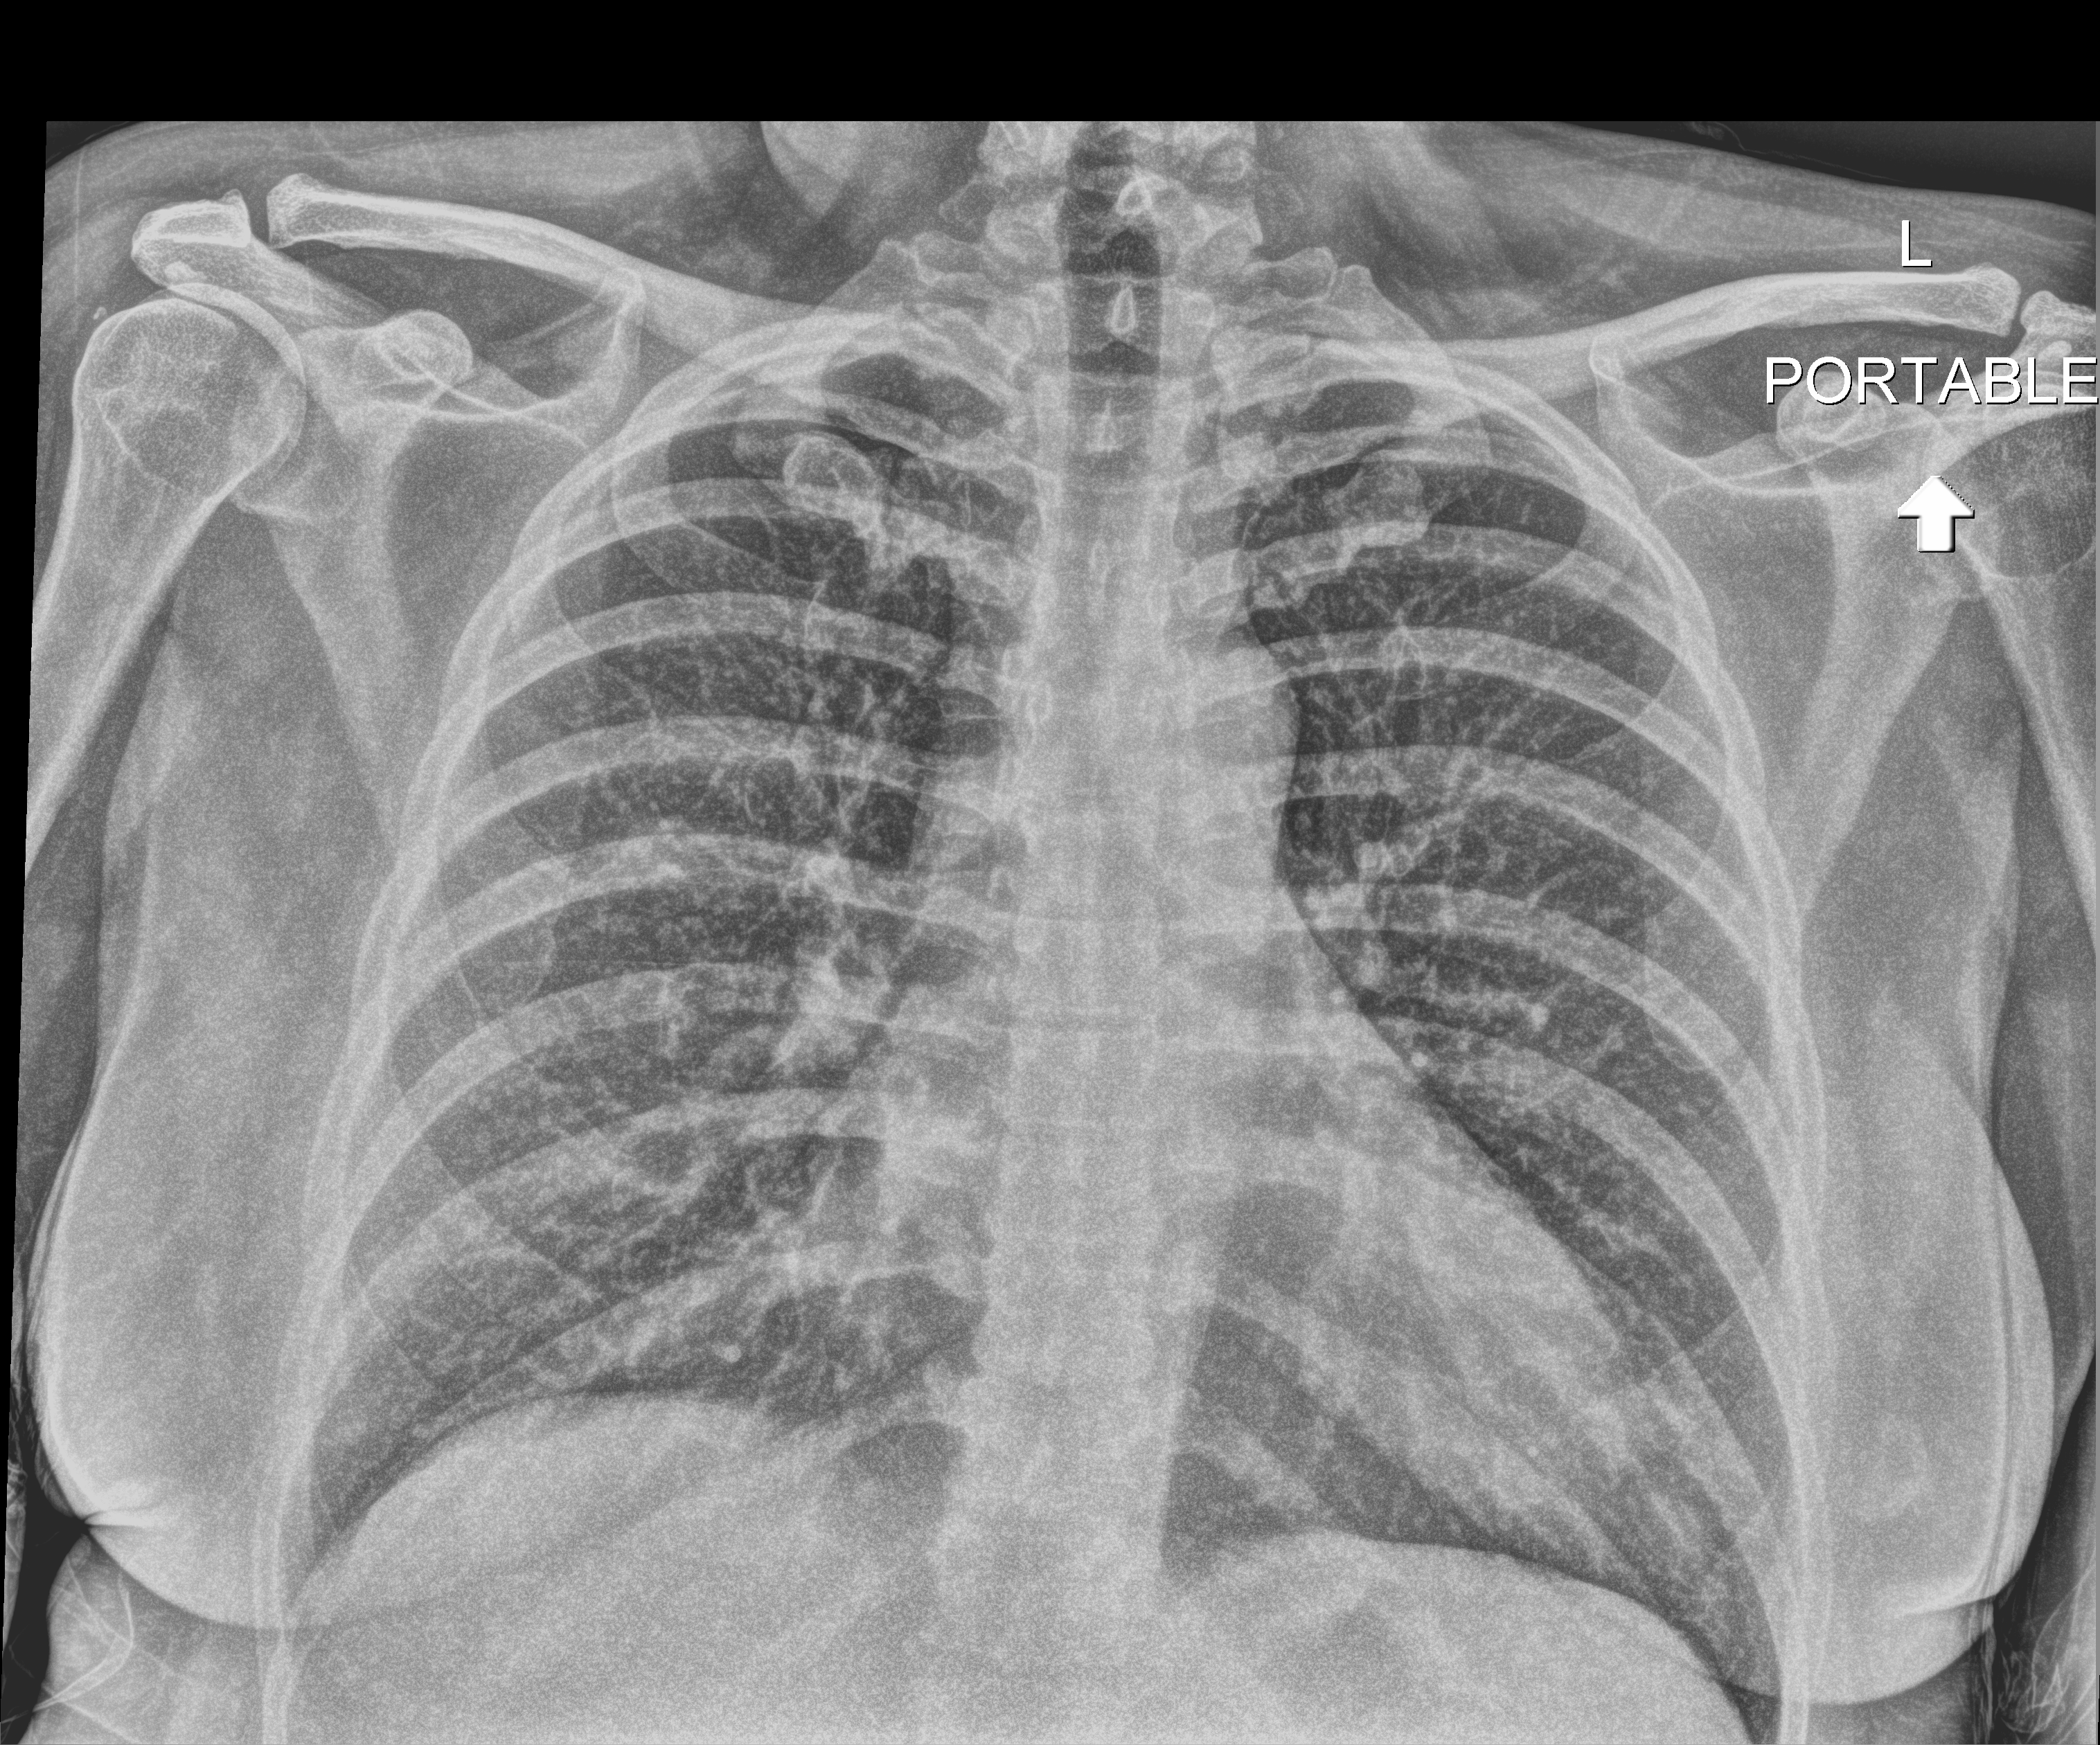
Chest radiograph; anteroposterior (AP) projection. Patient hospitalised with COVID-19; female, aged 18–59 years.
Hospital-stay facts (about this admission, not read from this image; timing relative to this image not recorded):
- admitted to intensive care during this hospital stay: no